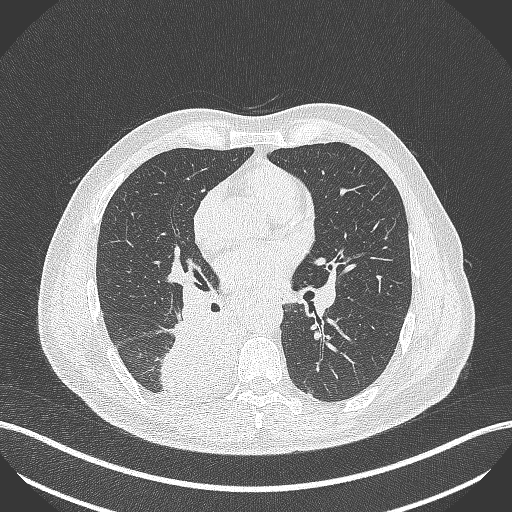
Chest CT, one axial slice. Slice 244 of 451 in the series (ordered by position). Reconstruction kernel B70f. 100 kVp. Lung window (W 1500 / L -600 HU). 1 mm slice thickness. 512 × 512 image matrix, field of view 400 × 400 mm. Patient: male, 61 years. Case-level facts recorded for this patient, not image findings: clinical TNM (as recorded): T1 N0 M0; histopathological grade: G3.
Outlined on this slice (rectangle marked by the reading radiologist):
- lung tumour (recorded histology: small cell carcinoma): box from (x=162, y=313) to (x=246, y=398) px